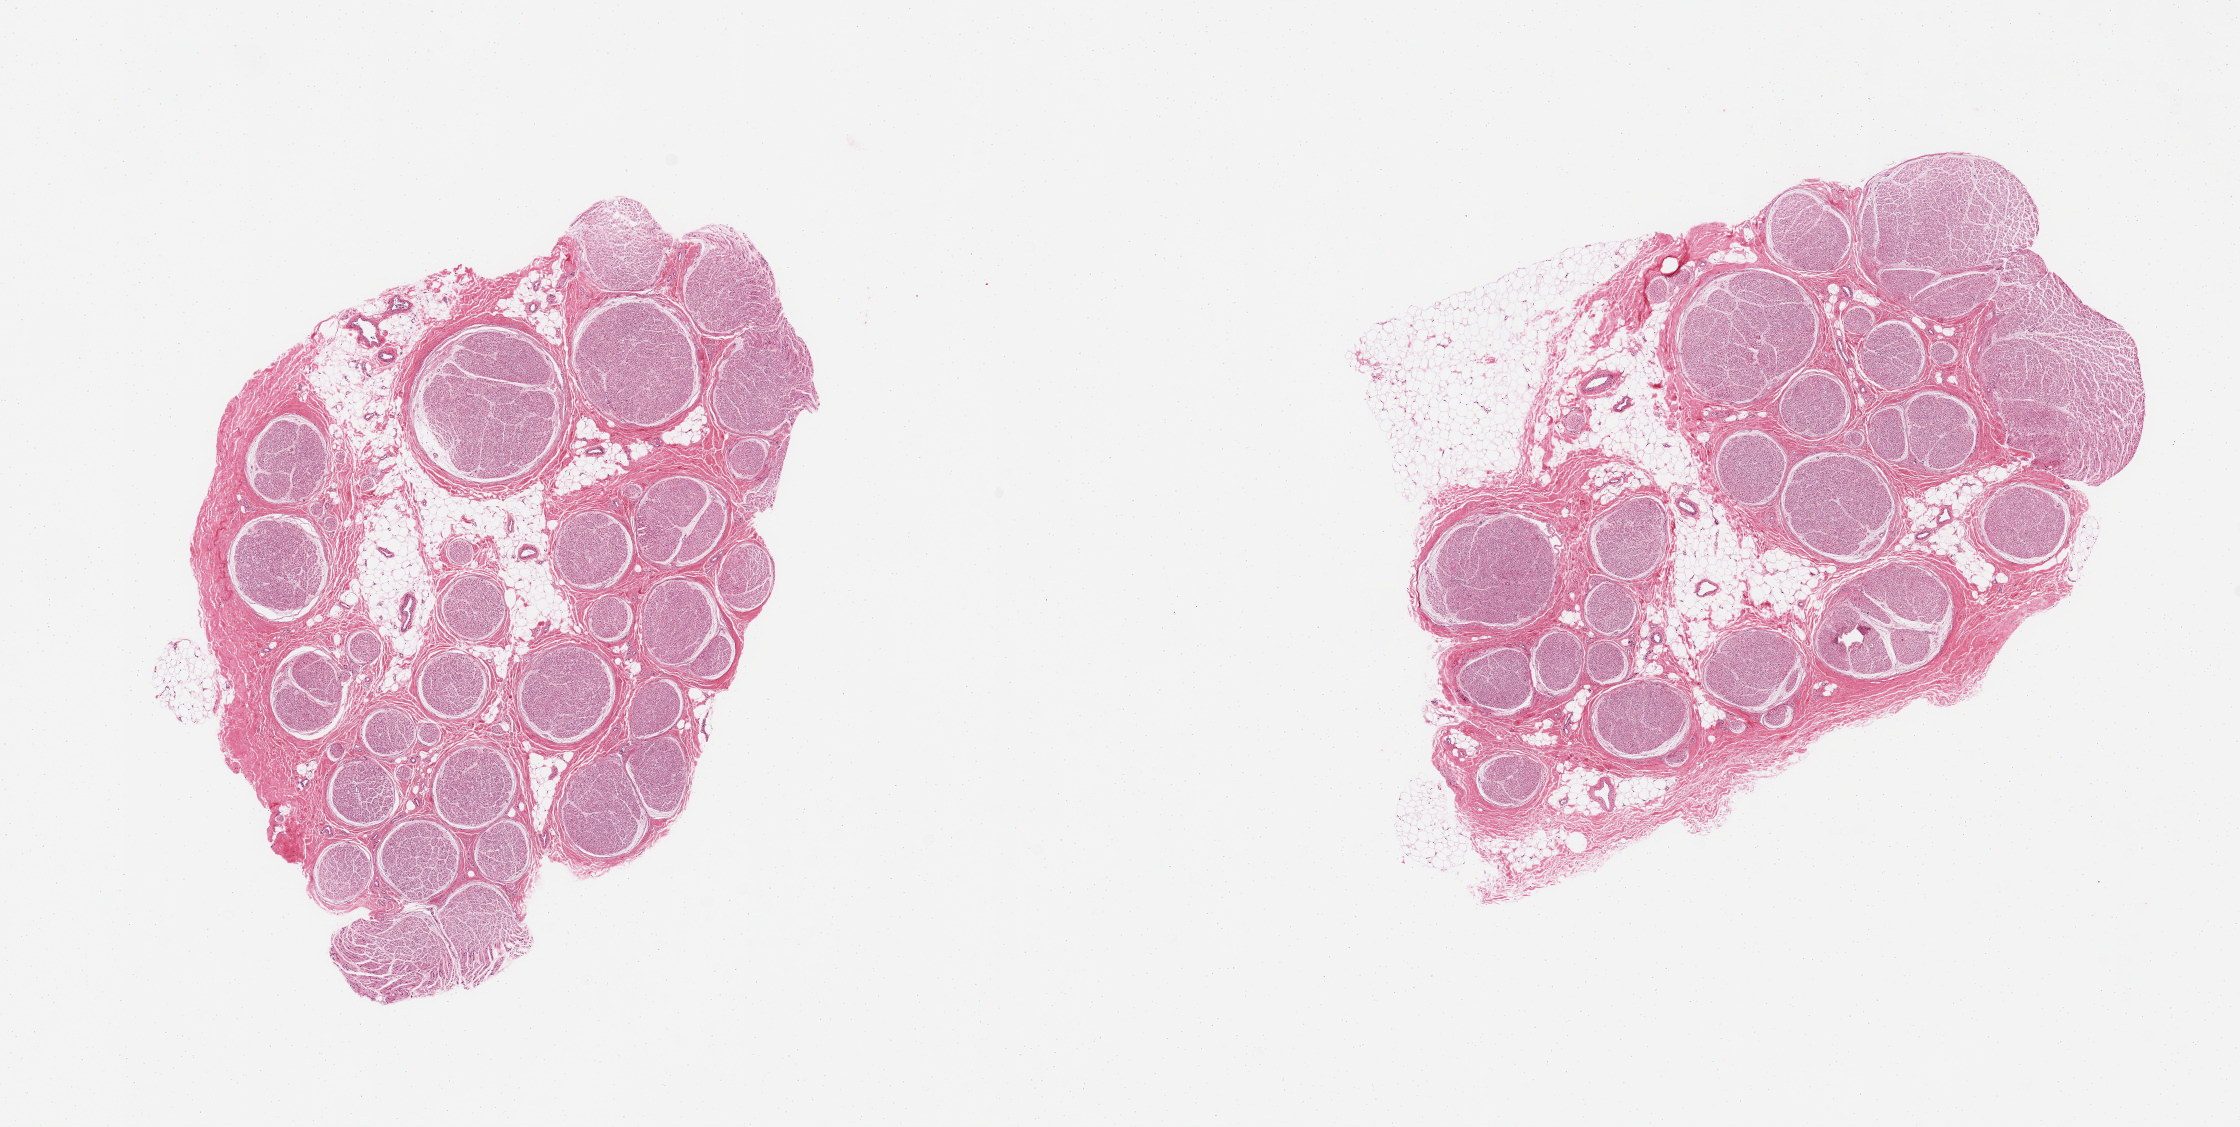
Whole-slide image, haematoxylin and eosin stain — whole scanned area (about 17.7 x 8.9 mm) shown as a low-resolution overview, PAXgene-fixed, paraffin-embedded tissue, target tissue: tibial nerve, donor tissue sample. Donor sex: male.
* pathologist's review note for this sample: 2 pieces: both have 20% internal fat; 1 has 20% external fat